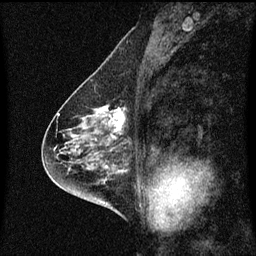
Breast MRI (dynamic contrast-enhanced), one sagittal slice. Position 33 of 60 along the scan axis. Dynamic contrast-enhanced series, image 2 of 3 at this slice position (ordered by acquisition). 1.5 T. TE 4.2 ms, TR 8.4 ms. 2 mm slice thickness. 256 × 256 image matrix, field of view 200 × 200 mm. Patient: female, 58 years.
Annotated regions visible in this slice (semi-automatically segmented with operator editing):
- analysis volume of interest (the breast-tissue region the enhancement analysis was run in; not a lesion): box from (x=86, y=106) to (x=131, y=143) px
- tumour enhancement mask (voxels above the 70 % enhancement threshold inside the analysis volume of interest): (x=88, y=106)–(x=126, y=141)